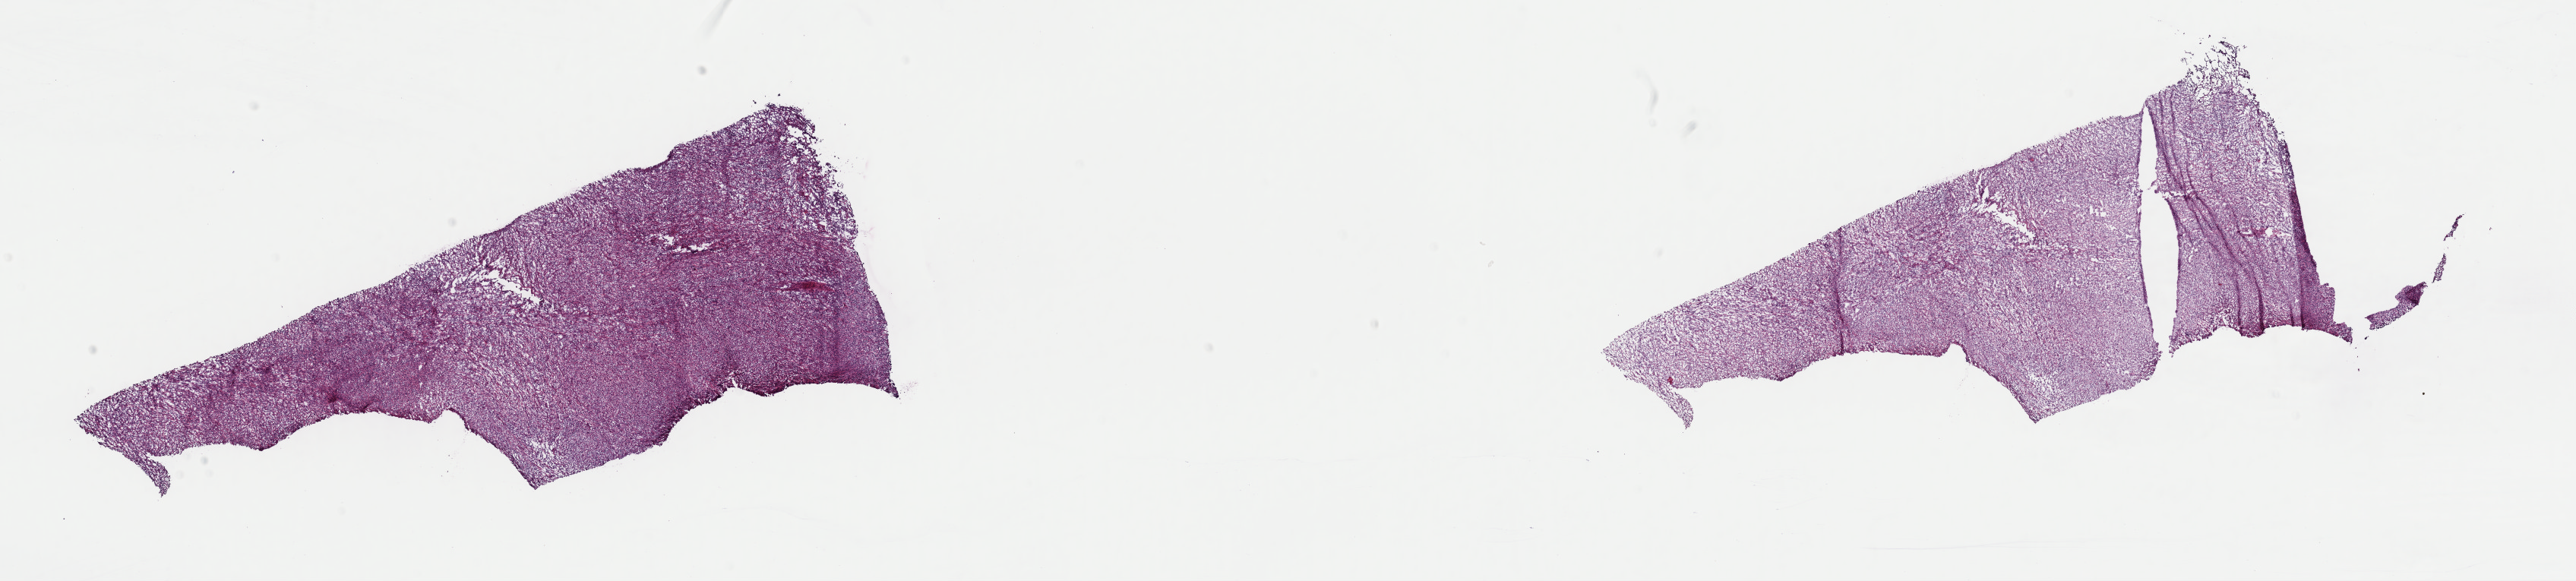
Whole-slide histology image, H&E — low-resolution overview of the scanned area, about 26.8 x 6.0 mm (acquisition: 40x scan), frozen section from the top of the tissue portion, retroperitoneum and peritoneum, primary tumour sample. Male, age 43 years at initial diagnosis. Composition of this section per pathologist review: tumour cells 100%, tumour nuclei 95%, normal cells 0%, stromal cells 0%, necrosis 0%. Infiltration values recorded for this section: lymphocyte infiltration 0%, monocyte infiltration 0%, neutrophil infiltration 0%.
Pathologic diagnosis: Leiomyosarcoma, NOS (retroperitoneum).